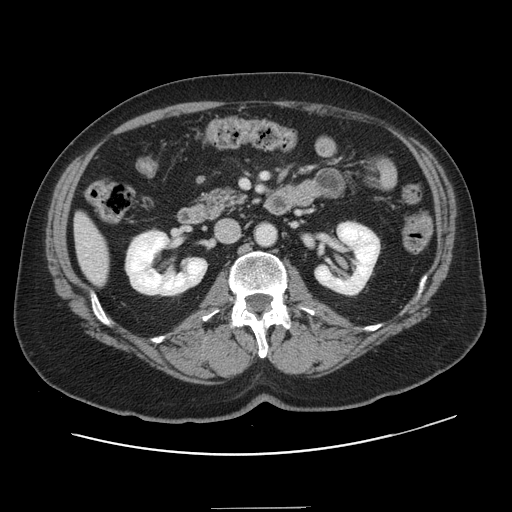
Contrast-enhanced abdominal CT, one axial slice. Slice 50 of 143 in the series (ordered by position). Intravenous contrast given. Soft-tissue window (W 400 / L 40 HU). 2.5 mm slice thickness. 512 × 512 image matrix, field of view 402 × 402 mm. Male patient, age 62 years. Case-level facts recorded for this patient, not image findings: diagnosis: colorectal cancer liver metastases, imaged before liver resection; multiple liver metastases: yes; largest metastasis: 2.7 cm; chemotherapy before resection: yes.
Outlined on this slice (outlined manually by an expert reader):
- liver: bounding box [x1, y1, x2, y2] px = [76, 217, 108, 284]